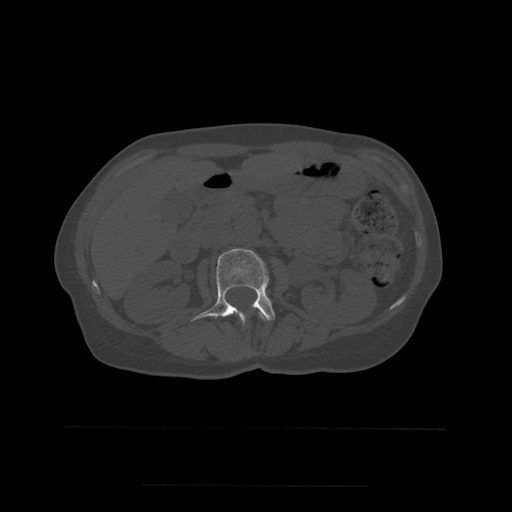
CT including the spine, one axial slice. Slice 216 of 544 in the series (ordered by position). Bone window (W 1800 / L 400 HU). 1.25 mm slice thickness. 512 × 512 image matrix, field of view 350 × 350 mm. Patient age 58 years. From the clinical record (not read from this slice): primary cancer: lung.
Annotated regions visible in this slice (semi-automatic segmentation, software-assisted and operator-edited):
- L1 vertebra: bounding box (x1, y1, x2, y2) in pixels: (258, 311, 266, 321)
- L2 vertebra: (191, 248, 275, 323)